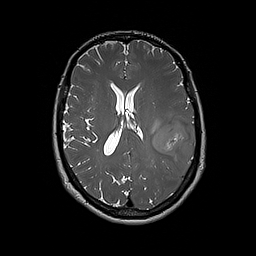
Brain MRI from a brain-tumour surgery series, one axial slice; slice 89 of 192 in the series (ordered by position); 256 × 256 image matrix, field of view 250 × 250 mm. Case-level facts recorded for this patient, not image findings: histopathology: Glioblastoma; WHO grade: 4; IDH mutation: no.
Outlined on this slice (manually delineated by an expert):
- tumour: bounding box (x1, y1, x2, y2) in pixels: (152, 116, 195, 167)